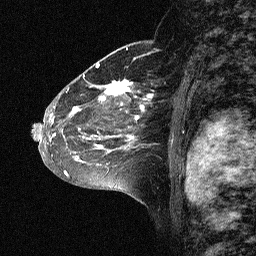
Breast MRI (dynamic contrast-enhanced), one sagittal slice; position 39 of 64 along the scan axis; dynamic contrast-enhanced study with each time point stored as its own series, time point 2 of 3 at this slice position (early post-contrast, ordered by acquisition time); 1.5 T; TE 4.5 ms, TR 11 ms; 2.06 mm slice thickness; 256 × 256 image matrix, field of view 200 × 200 mm. Patient: female, 46 years. From the clinical record (not read from this slice): setting: breast cancer imaged before/during neoadjuvant chemotherapy; receptor status: HER2-positive.
Annotated regions visible in this slice (semi-automatic segmentation, software-assisted and operator-edited):
- analysis volume of interest (the breast-tissue region the enhancement analysis was run in; not a lesion): bounding box (x1, y1, x2, y2) in pixels: (43, 72, 164, 177)
- tumour enhancement mask (voxels above the 90 % enhancement threshold inside the analysis volume of interest): (49, 78, 153, 177)